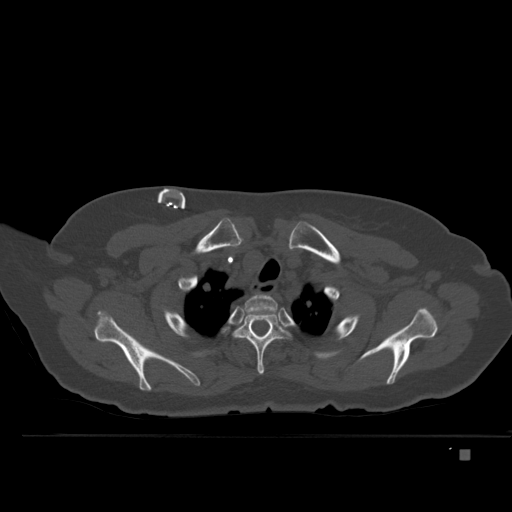
CT including the spine, one axial slice. Slice 393 of 477 in the series (ordered by position). Bone window (W 1800 / L 400 HU). 512 × 512 image matrix. Patient: female, 74 years. From the clinical record (not read from this slice): primary cancer: colon.
Outlined on this slice (semi-automatic segmentation, software-assisted and operator-edited):
- T1 vertebra: box from (x=230, y=294) to (x=278, y=324) px
- T2 vertebra: (x=223, y=306)–(x=294, y=374)